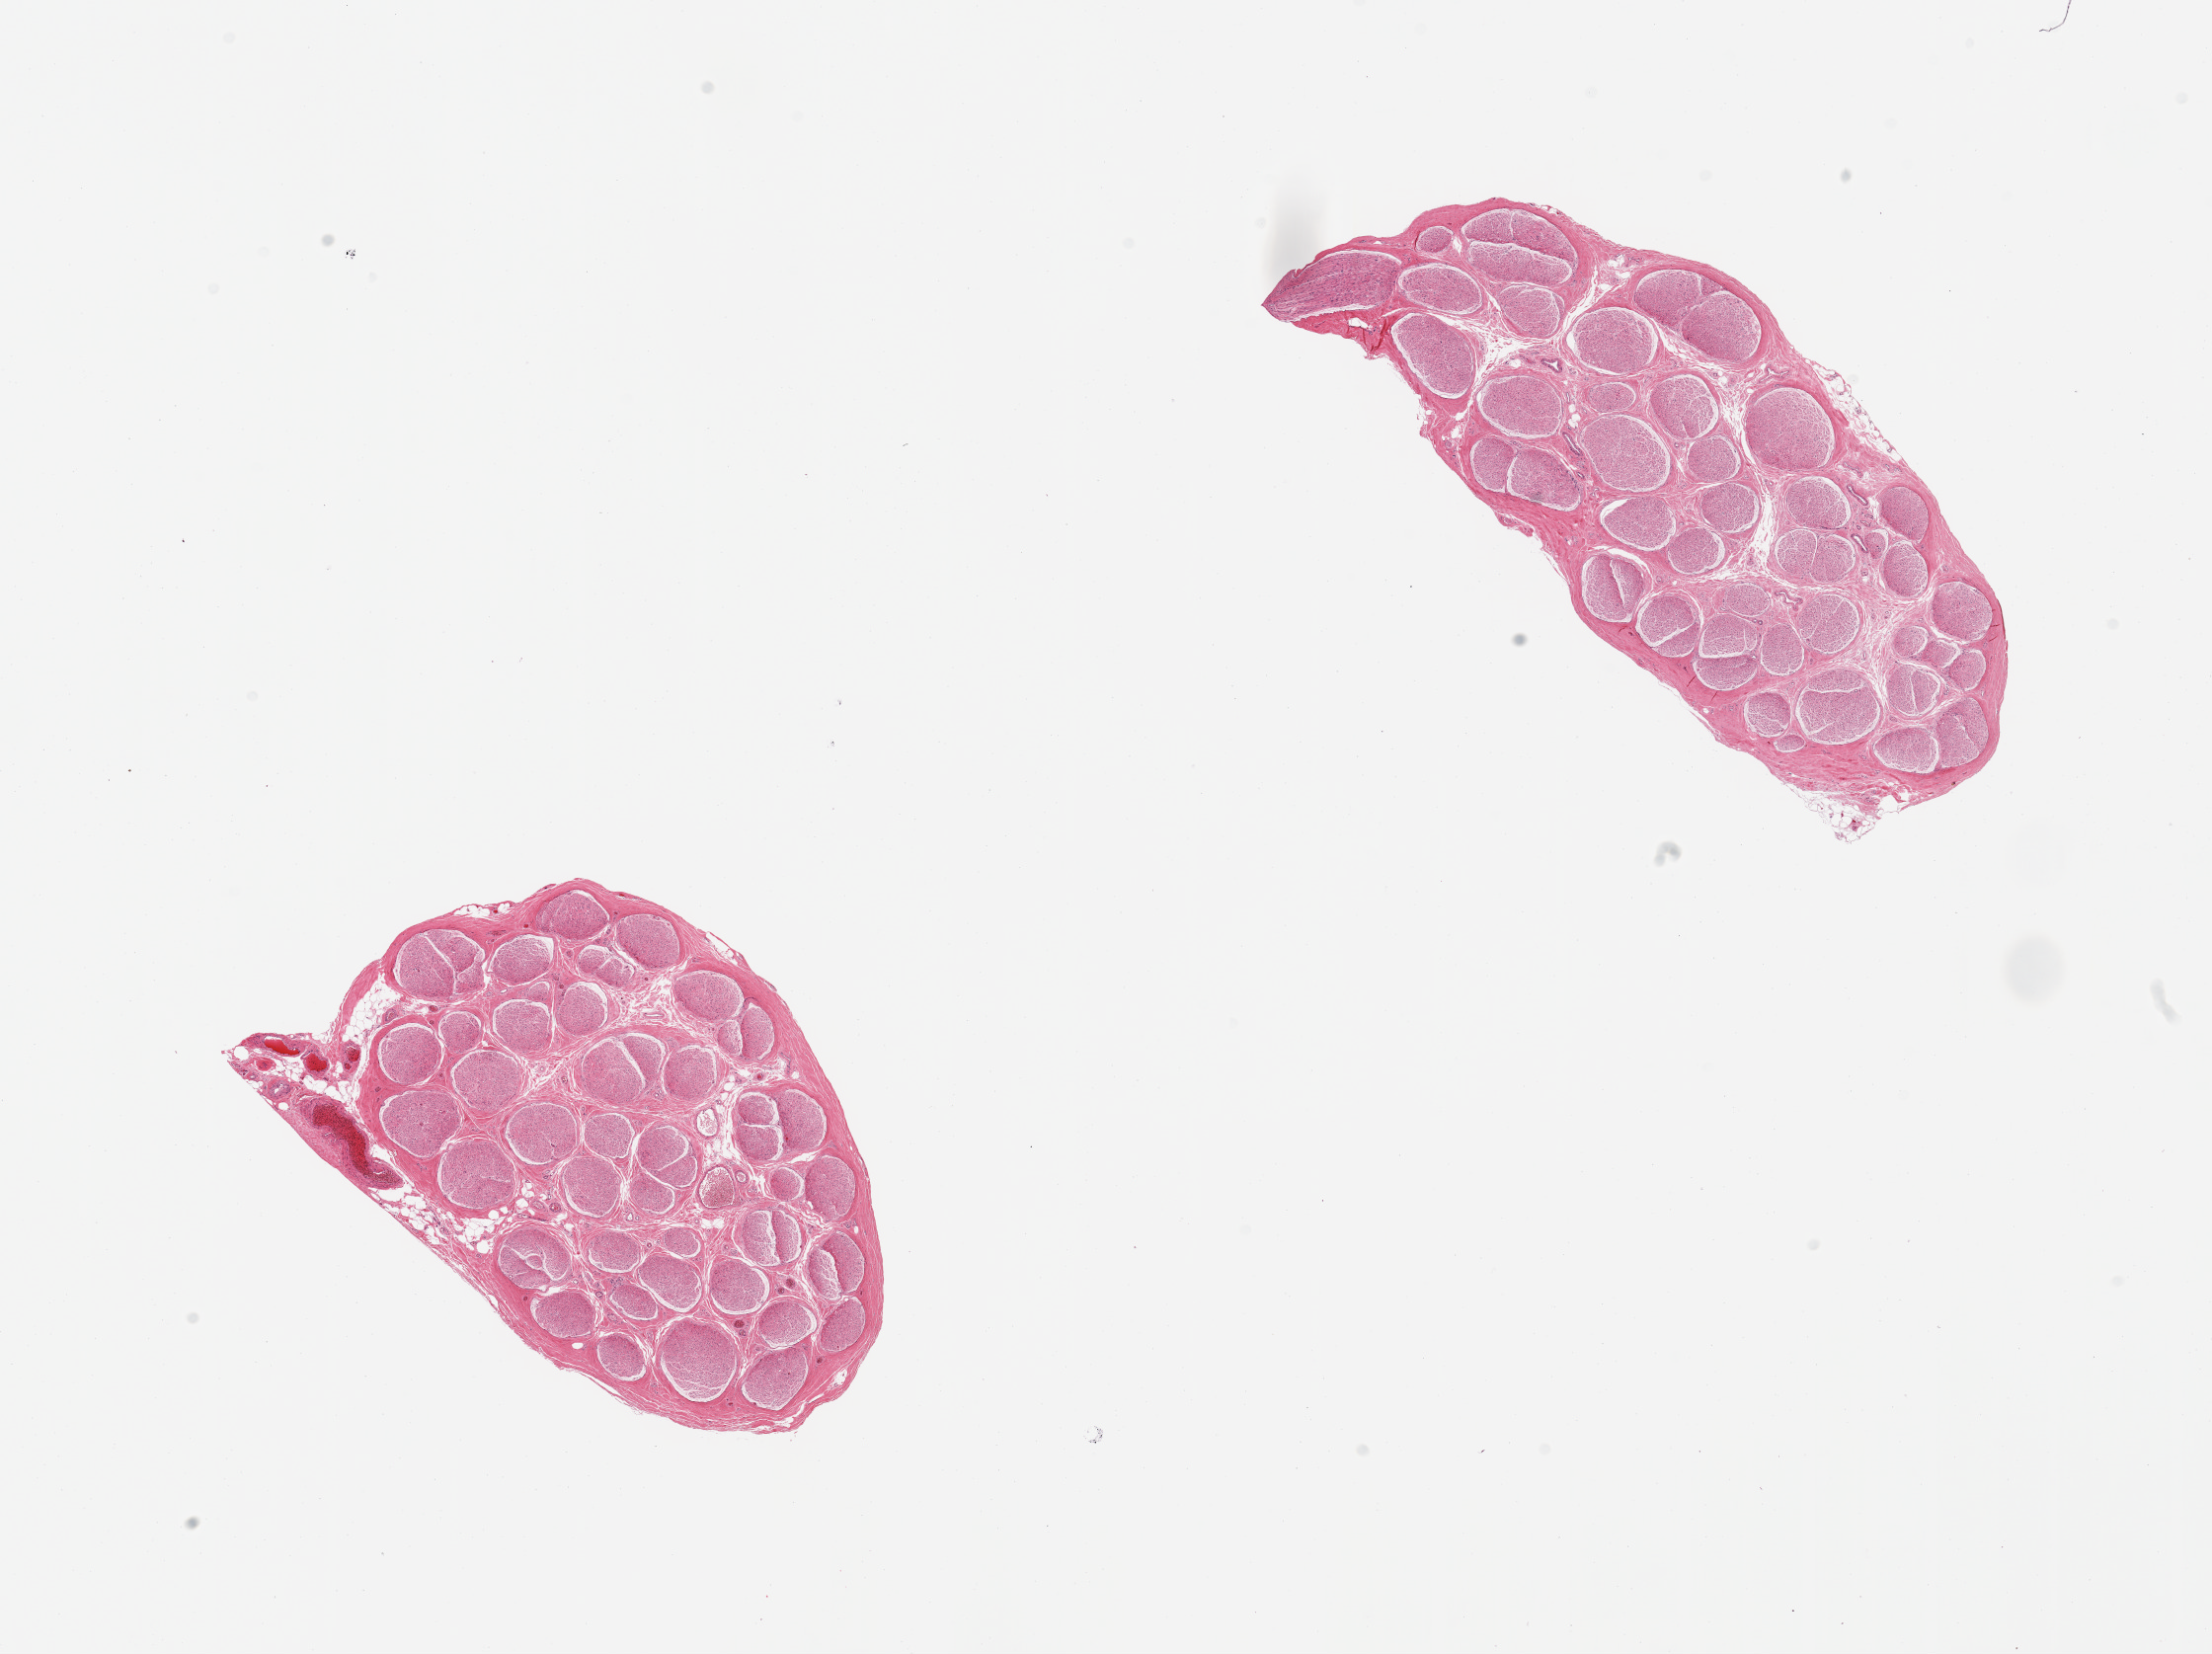
Digitized H&E-stained section — shown as a low-resolution overview of the whole scanned area (about 17.7 x 13.3 mm, from a 20x scan), PAXgene-fixed paraffin-embedded (PFPE) section, target tissue: tibial nerve, donor tissue sample.
Pathologist's review note for this sample: 2 pieces; well trimmed.